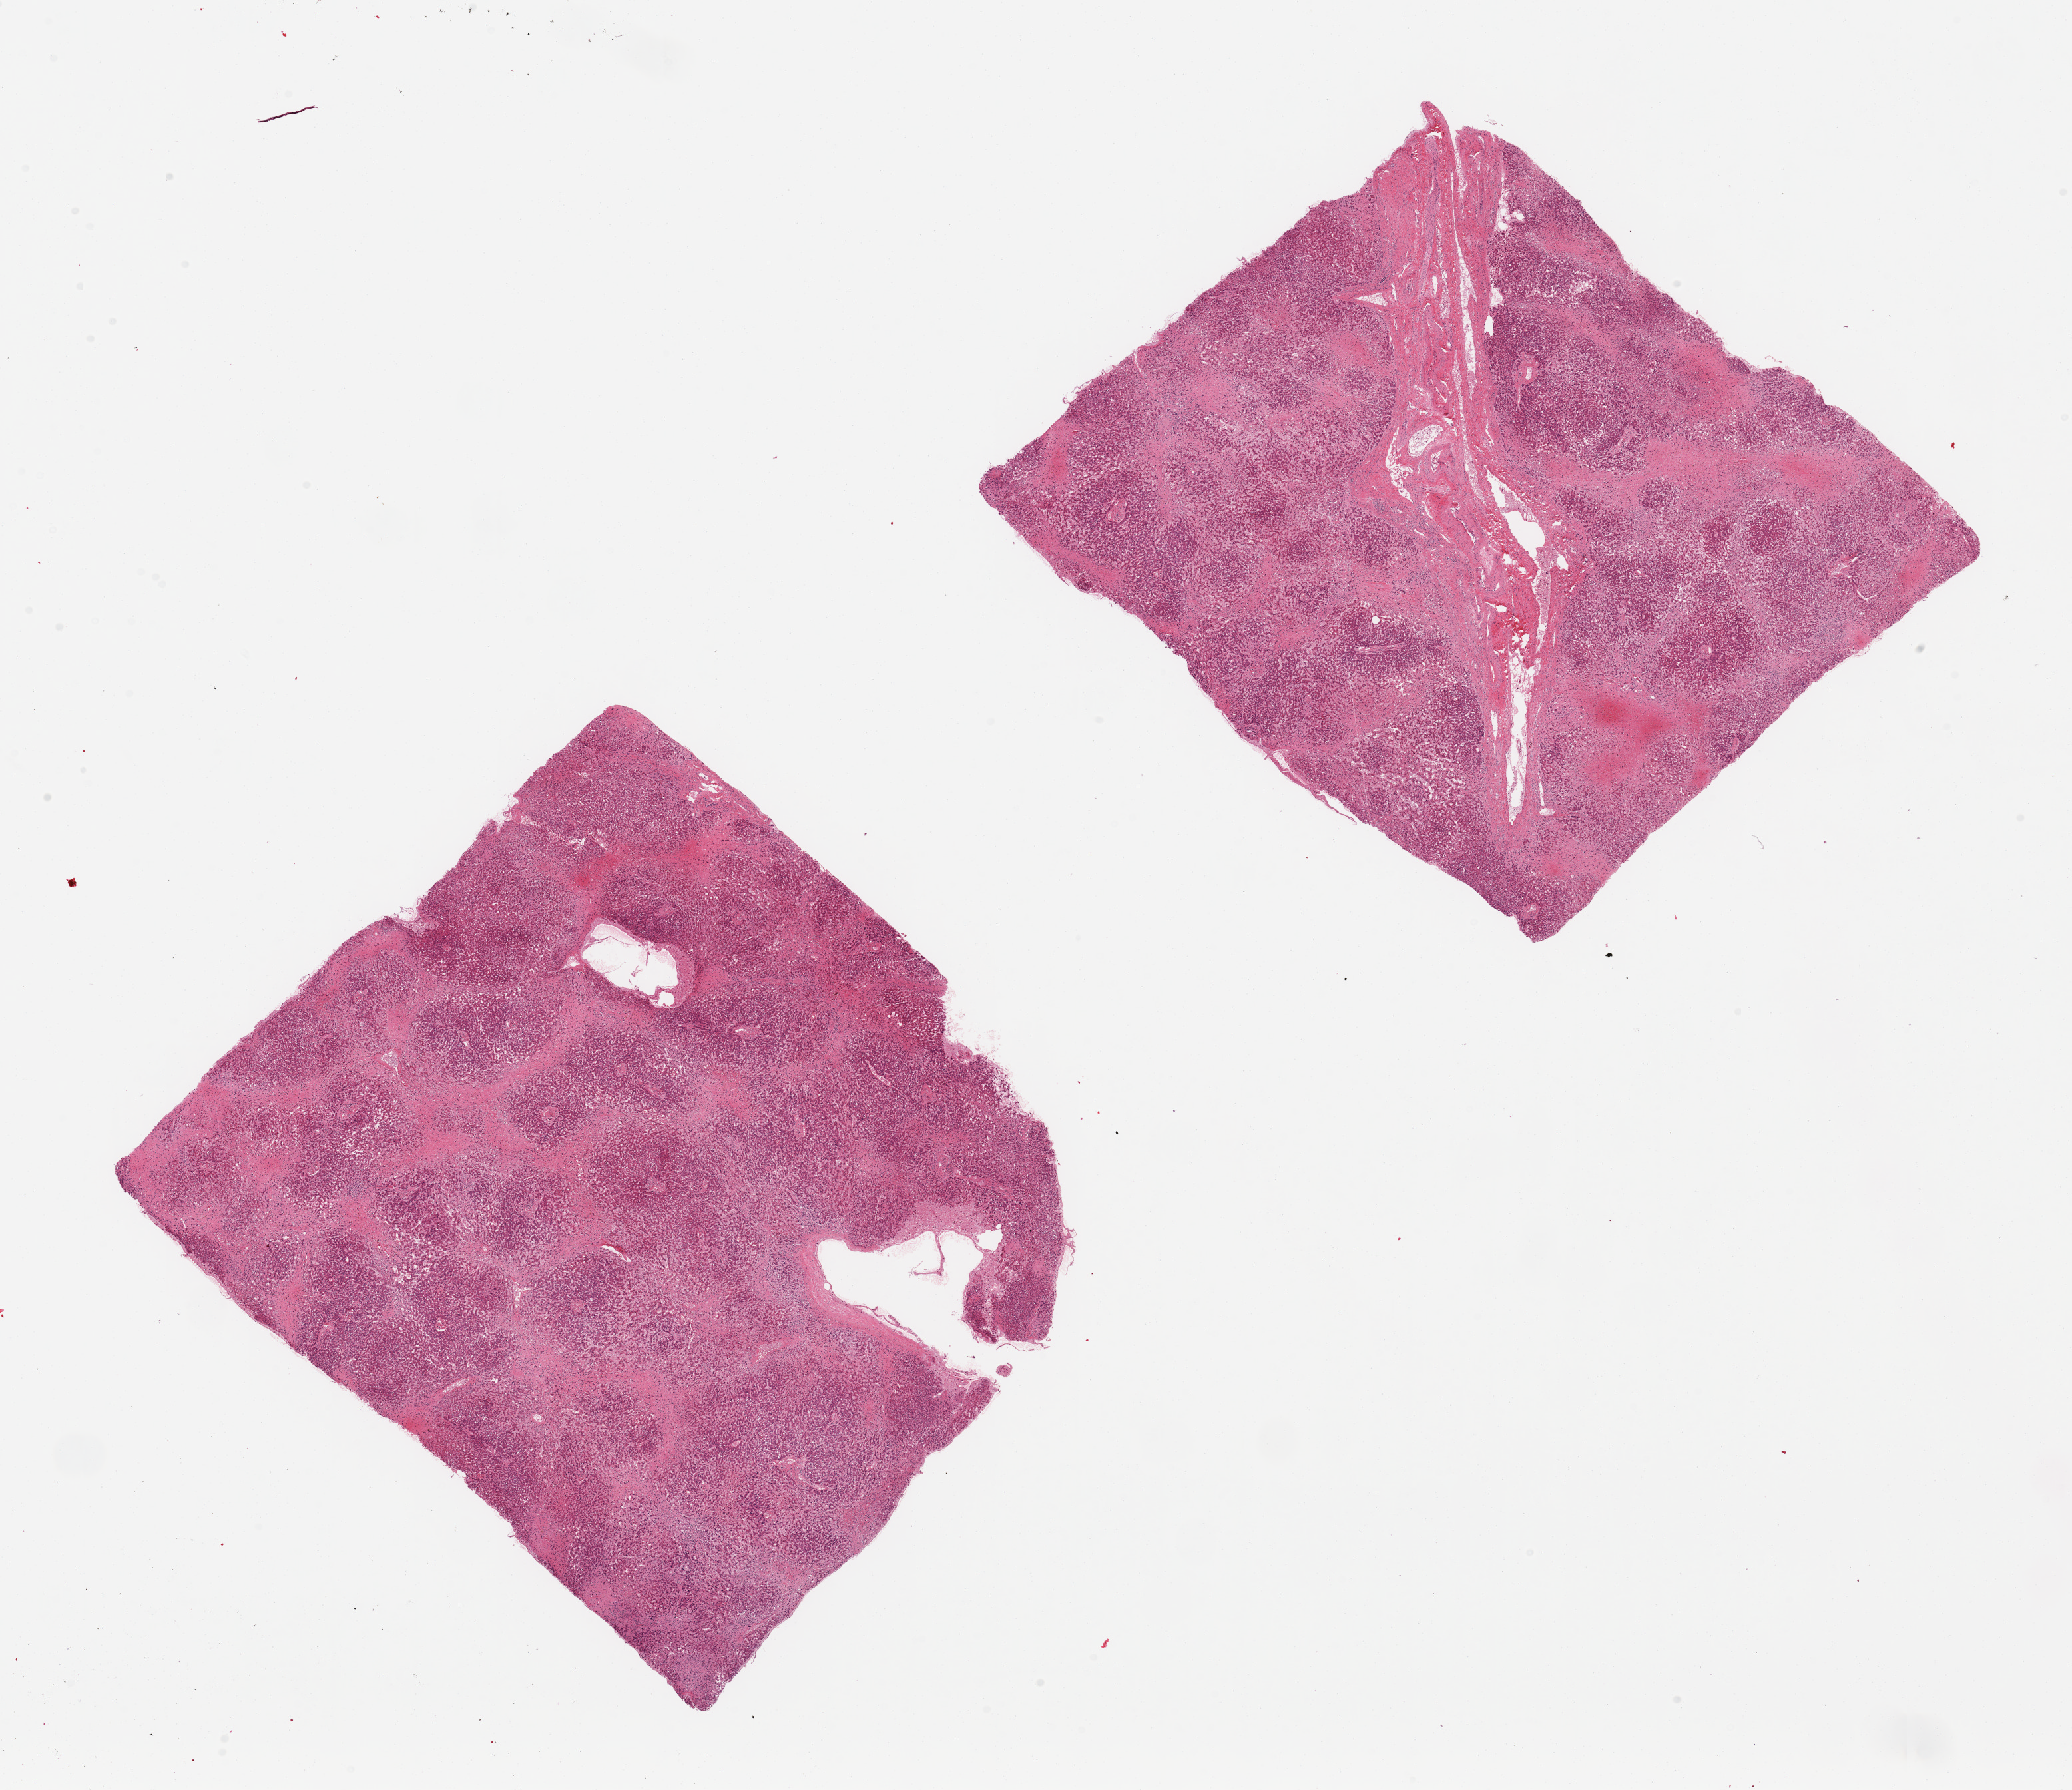
Digitized hematoxylin and eosin (H&E)-stained section — whole scanned area (about 24.6 x 21.3 mm) shown as a low-resolution overview, PAXgene-fixed, paraffin-embedded tissue, target tissue: liver, tissue donor sample. Male donor.
Review note (as recorded): 2 pieces; severe (50%) perilobular fibrosis consistent with cardiac cirrhosis; moderate macrovesicular steatosis.